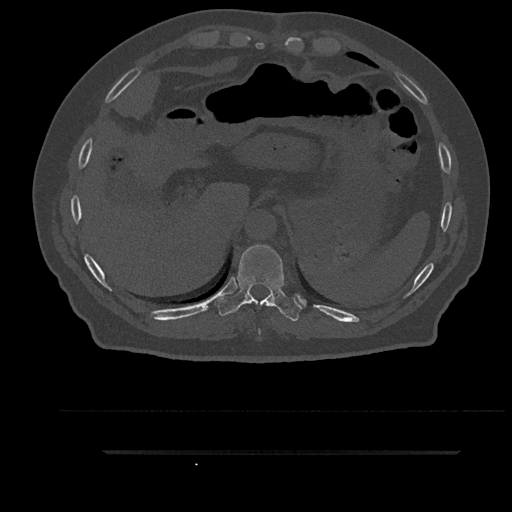
CT including the spine, one axial slice; slice 378 of 797 in the series (ordered by position); reconstruction kernel Br40s/3; 120 kVp; bone window (W 1800 / L 400 HU); 512 × 512 image matrix. Patient: male, 63 years. From the clinical record (not read from this slice): primary cancer: renal.
Structures marked on this image (semi-automatically segmented with operator editing):
- T10 vertebra: bounding box <218,245,303,322> (left, top, right, bottom; pixels)
- T9 vertebra: <258,302,266,335>